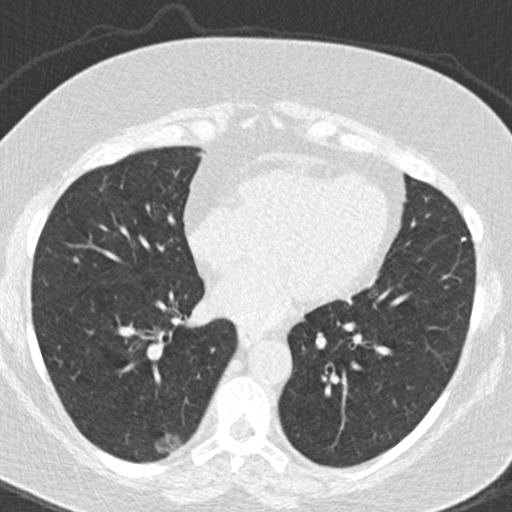
Low-dose screening chest CT, one axial slice; position 71 of 177 along the scan axis; reconstruction kernel B30f; 120 kVp; lung window (W 1500 / L -600 HU); 2 mm slice thickness; 512 × 512 image matrix, field of view 300 × 300 mm.
Outlined on this slice (outlined manually by an expert reader):
- lesion 1 (tumor, lower lobe of right lung): bounding box [x1, y1, x2, y2] px = [155, 433, 182, 452]